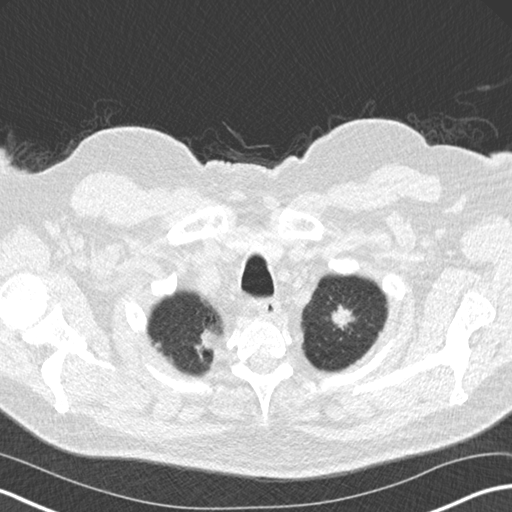
Low-dose screening chest CT, one axial slice; 120 kVp; lung window (W 1500 / L -600 HU); 512 × 512 image matrix, field of view 351 × 351 mm.
Structures marked on this image (manually delineated by an expert):
- lesion 1 (tumor, upper lobe of left lung): box from (x=332, y=304) to (x=355, y=330) px